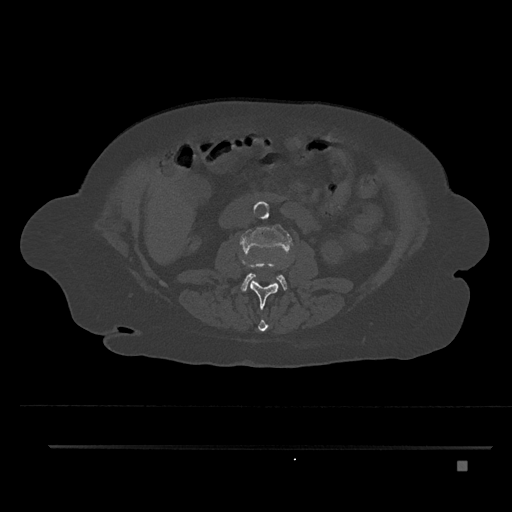
CT including the spine, one axial slice; position 161 of 797 along the scan axis; reconstruction kernel Br40s/3; 120 kVp; bone window (W 1800 / L 400 HU); 0.5 mm slice thickness; 512 × 512 image matrix, field of view 437 × 437 mm. Patient: female, 76 years. Case-level facts recorded for this patient, not image findings: primary cancer: lung.
Structures marked on this image (semi-automatically segmented with operator editing):
- L1 vertebra: bounding box [x1, y1, x2, y2] px = [258, 320, 268, 332]
- L2 vertebra: [241, 259, 281, 309]
- L3 vertebra: [240, 224, 292, 292]